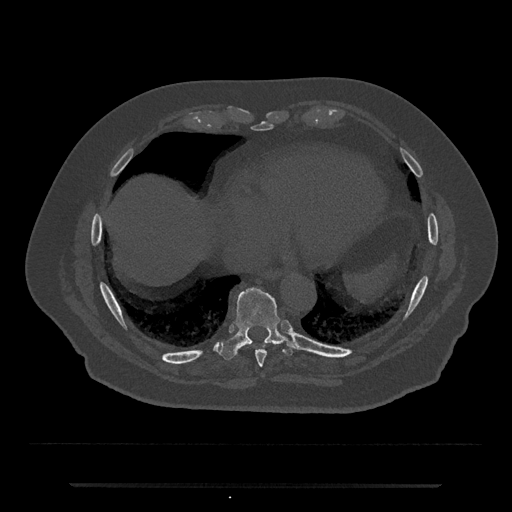
CT including the spine, one axial slice; slice 774 of 797 in the series (ordered by position); reconstruction kernel Br40s/3; 120 kVp; bone window (W 1800 / L 400 HU); 0.5 mm slice thickness; 512 × 512 image matrix, field of view 434 × 434 mm. Patient: male, 80 years. Case-level facts recorded for this patient, not image findings: primary cancer: prostate; vertebrae with lytic lesions (as recorded): L1, T11.
Structures marked on this image (semi-automatic segmentation, software-assisted and operator-edited):
- T8 vertebra: box from (x=256, y=350) to (x=266, y=368) px
- T9 vertebra: (x=217, y=287)–(x=299, y=360)